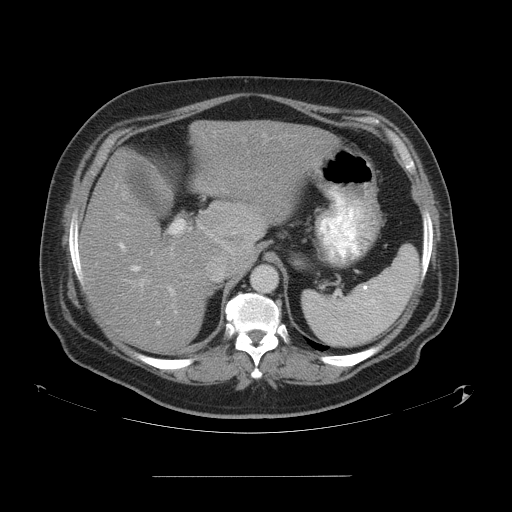
Contrast-enhanced abdominal CT, one axial slice; 120 kVp; soft-tissue window (W 400 / L 40 HU); 5 mm slice thickness; 512 × 512 image matrix, field of view 480 × 480 mm. Male patient, age 63 years. From the clinical record (not read from this slice): diagnosis: colorectal cancer liver metastases, imaged before liver resection; multiple liver metastases: no; largest metastasis: 4.2 cm; chemotherapy before resection: yes.
Annotated regions visible in this slice (outlined manually by an expert reader):
- hepatic veins: bounding box (x1, y1, x2, y2) in pixels: (117, 211, 226, 271)
- liver: (81, 121, 333, 351)
- planned liver remnant (the part of the liver to remain after resection): (81, 194, 210, 352)
- portal vein (with intrahepatic branches): (120, 219, 191, 324)
- liver metastasis: (217, 222, 250, 255)